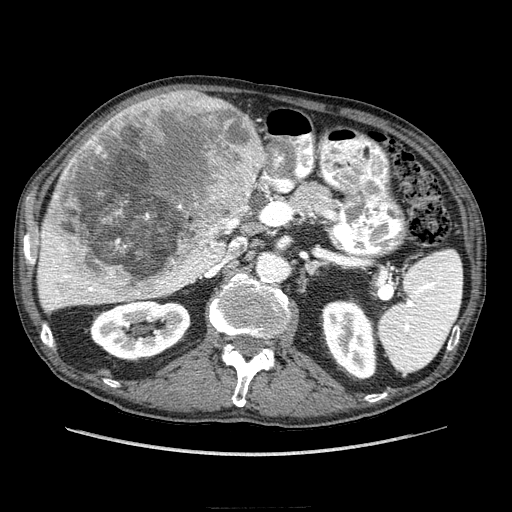
Contrast-enhanced abdominal CT (liver protocol), one axial slice. Reconstruction kernel STANDARD. Soft-tissue window (W 400 / L 40 HU). 2.5 mm slice thickness. 512 × 512 image matrix, field of view 380 × 380 mm. From the clinical record (not read from this slice): diagnosis: hepatocellular carcinoma (patient treated with transarterial chemoembolisation; whether this scan precedes or follows treatment is not stated here); TNM stage (as recorded): Stage-IIIA; Child-Pugh class: A.
Annotated regions visible in this slice (semi-automatically segmented with operator editing):
- liver parenchyma outside the tumour (the mass and vessels are separate outlines, so this box may not span the whole liver): bounding box [x1, y1, x2, y2] px = [38, 101, 264, 312]
- mass: [40, 90, 264, 300]
- liver vessels: [41, 262, 169, 307]